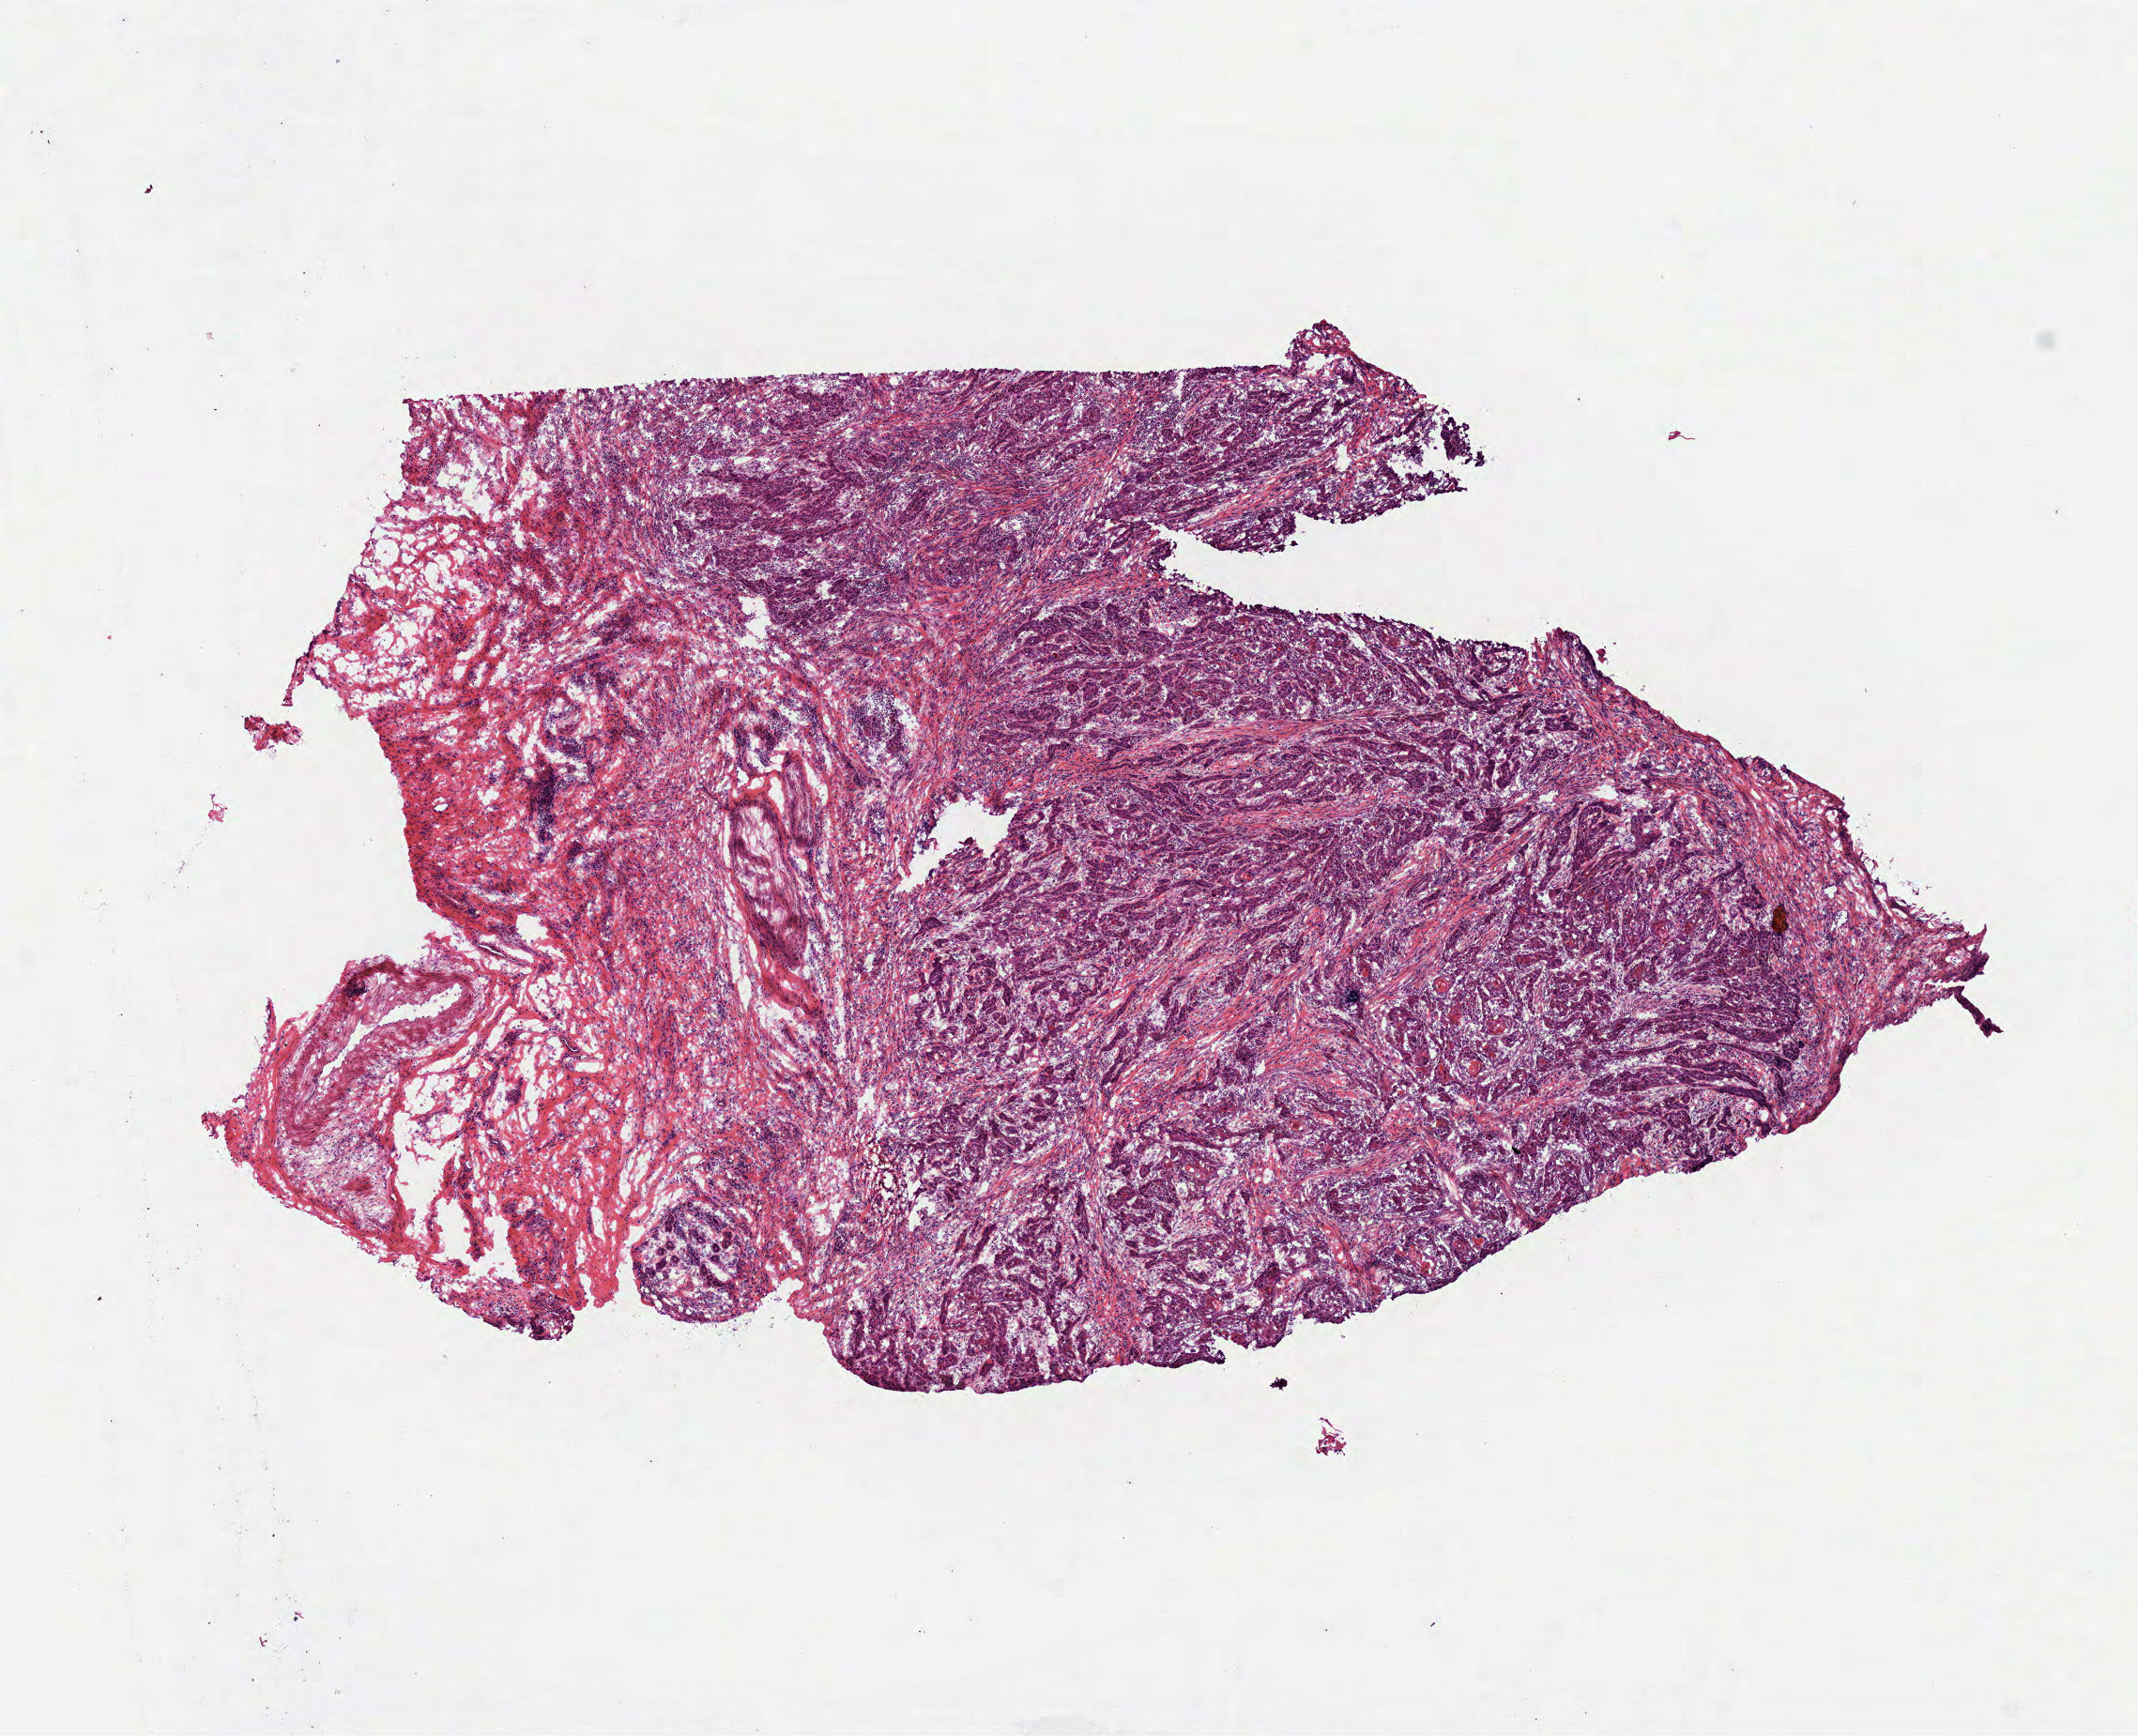
H&E-stained whole-slide image, whole scanned area (about 9.2 x 7.5 mm) shown as a low-resolution overview. Frozen section. Sample: primary tumour, head and neck. Female, age 73 years at initial diagnosis. Histologic grade: G3 (poorly differentiated). Slide review estimates, as recorded: tumour cells 73%, tumour nuclei 71%, normal cells 0%, stromal cells 26%, necrosis 1%. Infiltration values recorded for this section: lymphocyte infiltration 10%, monocyte infiltration 0%, neutrophil infiltration 10%.
Histologic diagnosis: Squamous cell carcinoma, NOS (overlapping lesion of lip, oral cavity and pharynx). AJCC pathologic stage: II.